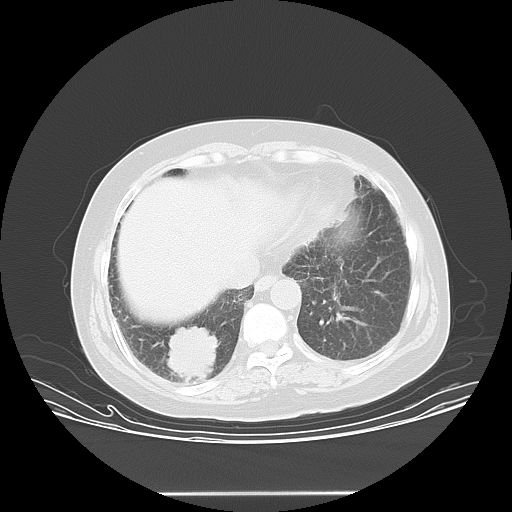
Chest CT, one axial slice. Position 8 of 45 along the scan axis. 120 kVp. Lung window (W 1500 / L -600 HU). 5 mm slice thickness. 512 × 512 image matrix, field of view 408 × 408 mm. Female patient, age 55 years. Case-level facts recorded for this patient, not image findings: clinical TNM (as recorded): T2 N0 M1b.
Outlined on this slice (bounding box drawn by a radiologist):
- lung tumour (recorded histology: squamous cell carcinoma): bounding box (x1, y1, x2, y2) in pixels: (157, 321, 224, 403)